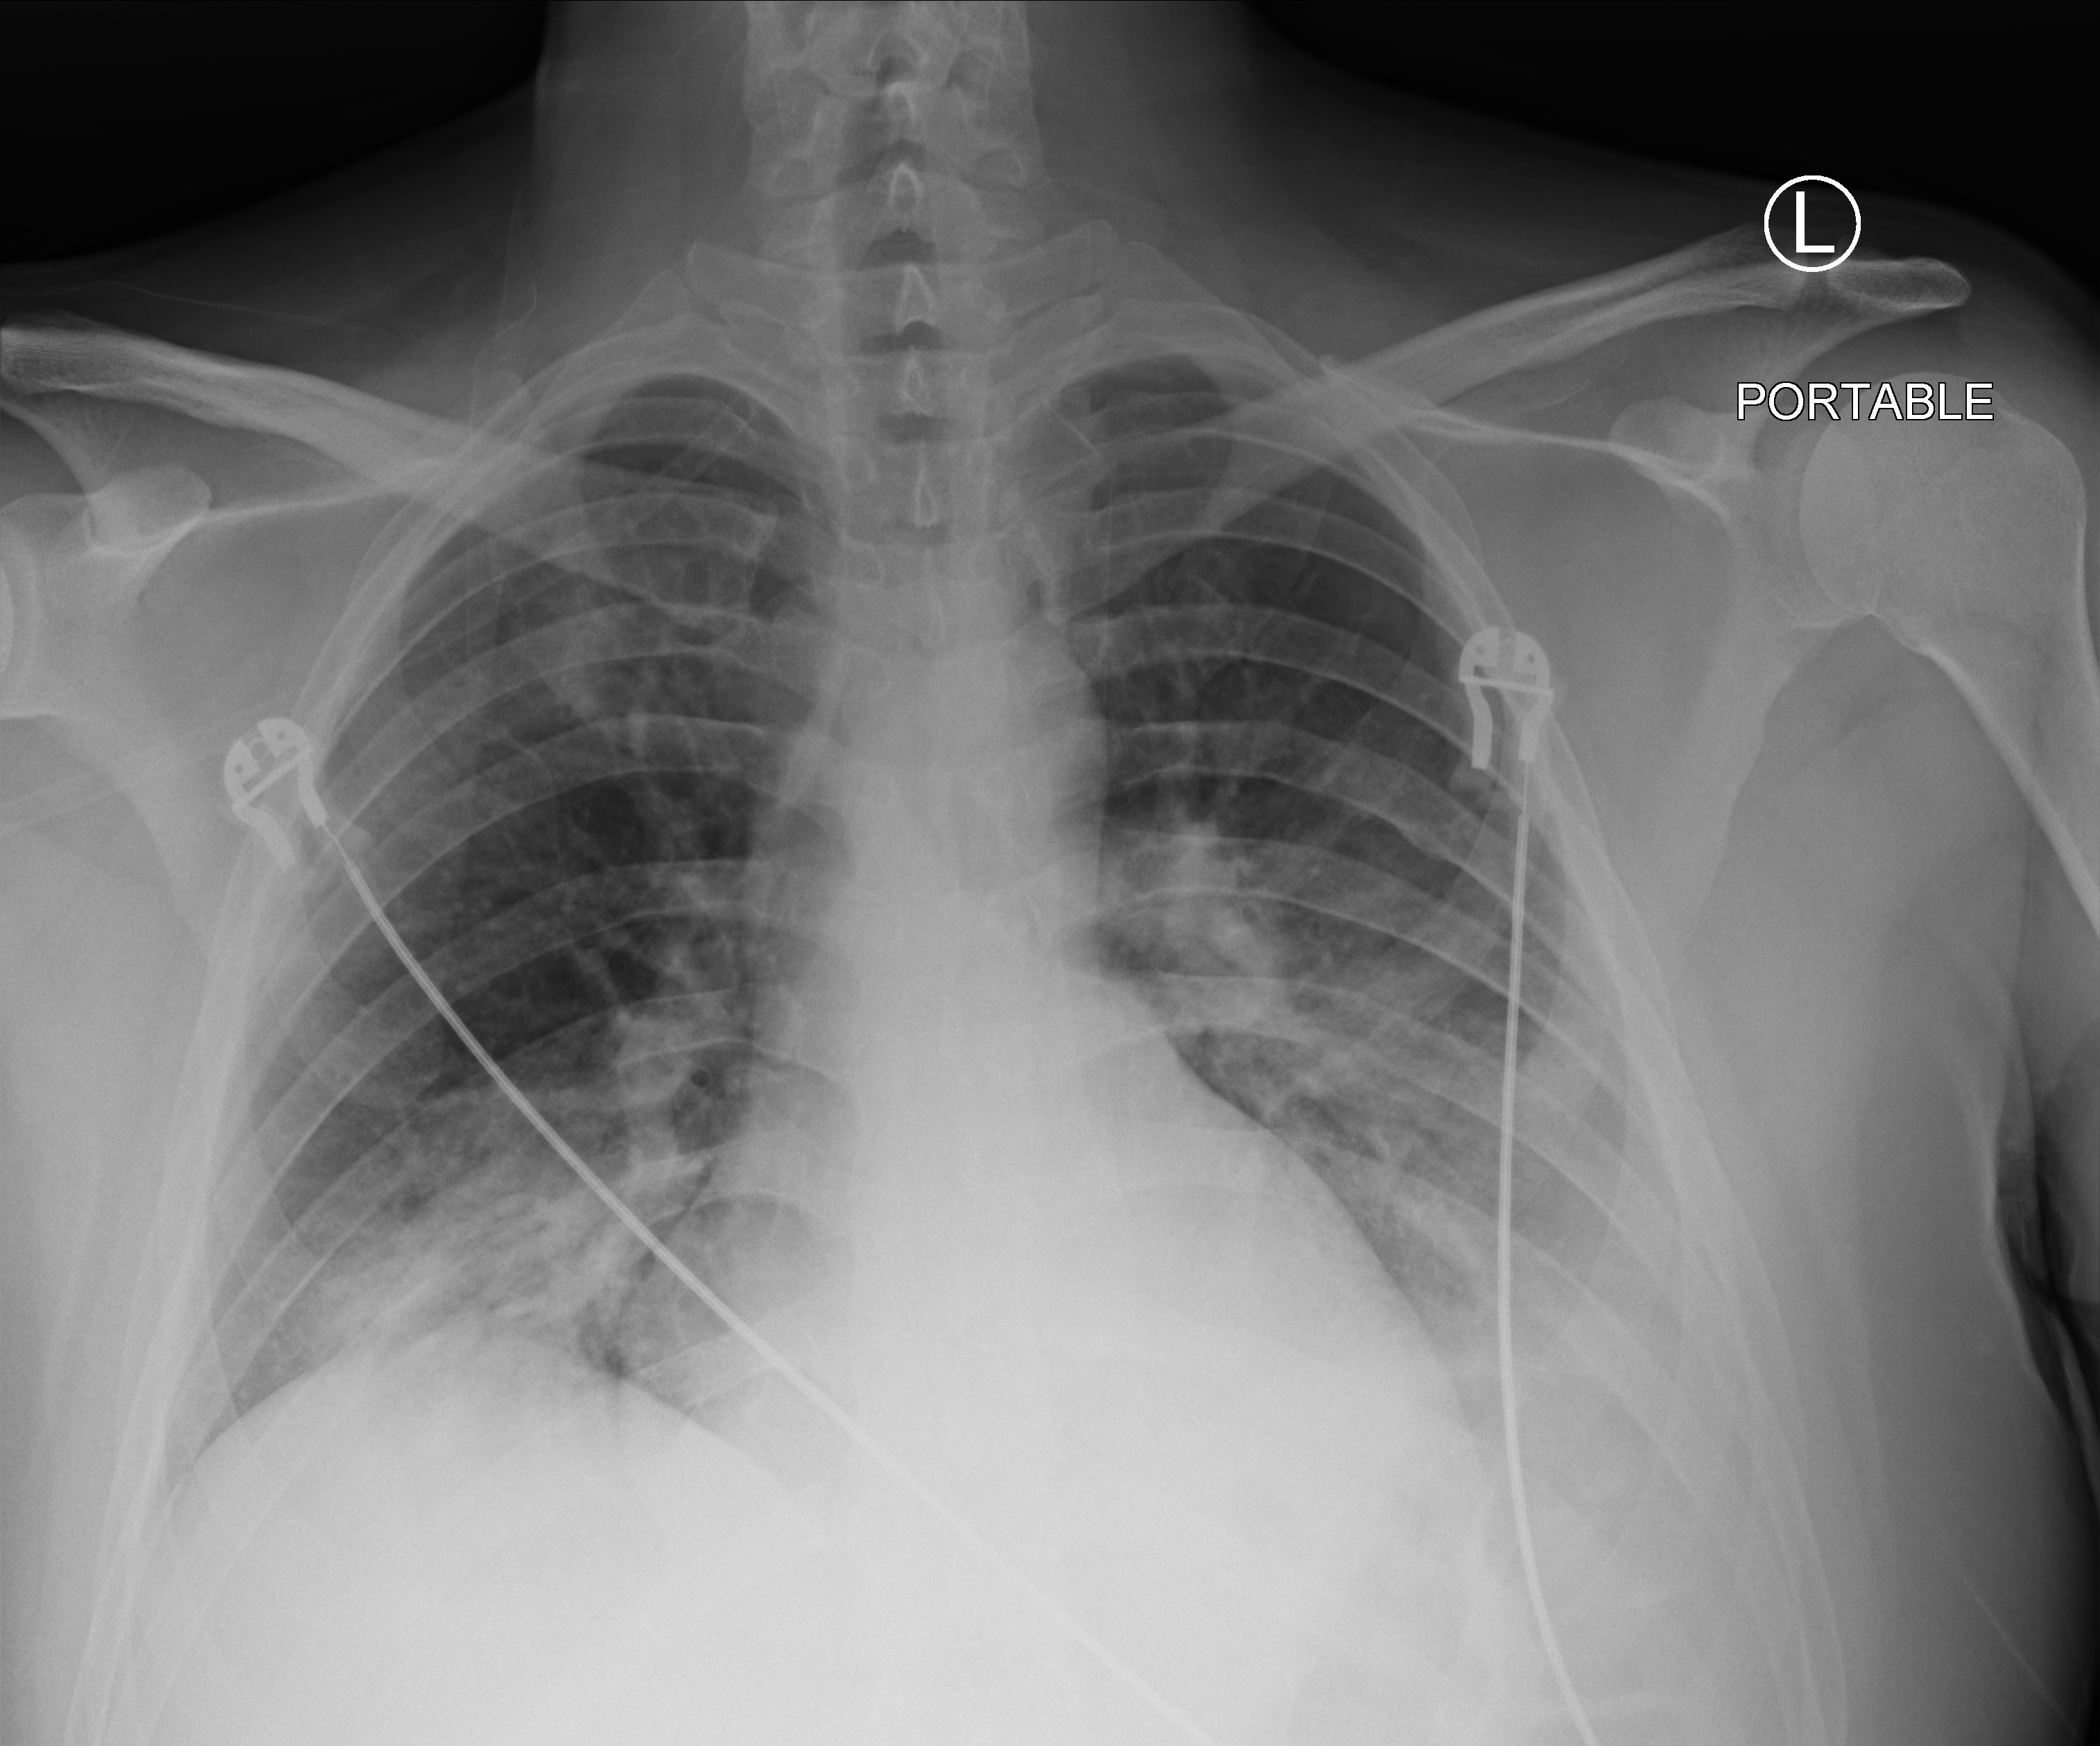
Bedside chest radiograph (computed radiography), anteroposterior (AP) projection. Male patient hospitalised with COVID-19, age 18–59 years.
From the hospital-stay record, not from the radiograph (when in the stay this image was taken is not recorded): length of hospital stay: 4 days; admitted to intensive care during this hospital stay: no; mechanically ventilated during this hospital stay: no.